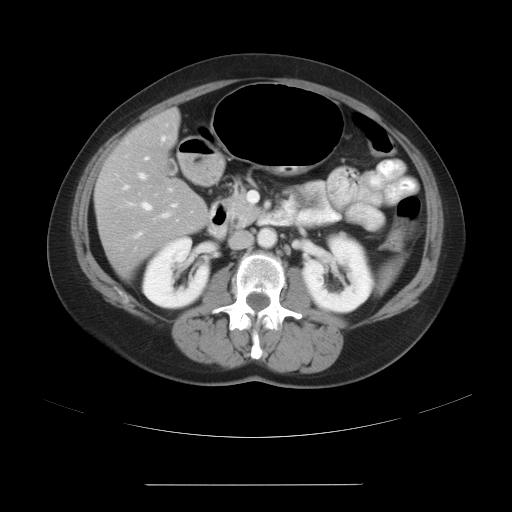
Contrast-enhanced abdominal CT, one axial slice. Slice 12 of 27 in the series (ordered by position). Intravenous contrast given. Soft-tissue window (W 400 / L 40 HU). 7.5 mm slice thickness. 512 × 512 image matrix. Female patient, age 58 years. Case-level facts recorded for this patient, not image findings: diagnosis: colorectal cancer liver metastases, imaged before liver resection; multiple liver metastases: yes; largest metastasis: 1.9 cm; disease in both lobes: yes.
Annotated regions visible in this slice (expert manual segmentation):
- hepatic veins: bounding box (x1, y1, x2, y2) in pixels: (119, 200, 153, 239)
- liver: (96, 110, 207, 275)
- planned liver remnant (the part of the liver to remain after resection): (97, 111, 202, 207)
- portal vein (with intrahepatic branches): (97, 135, 253, 226)